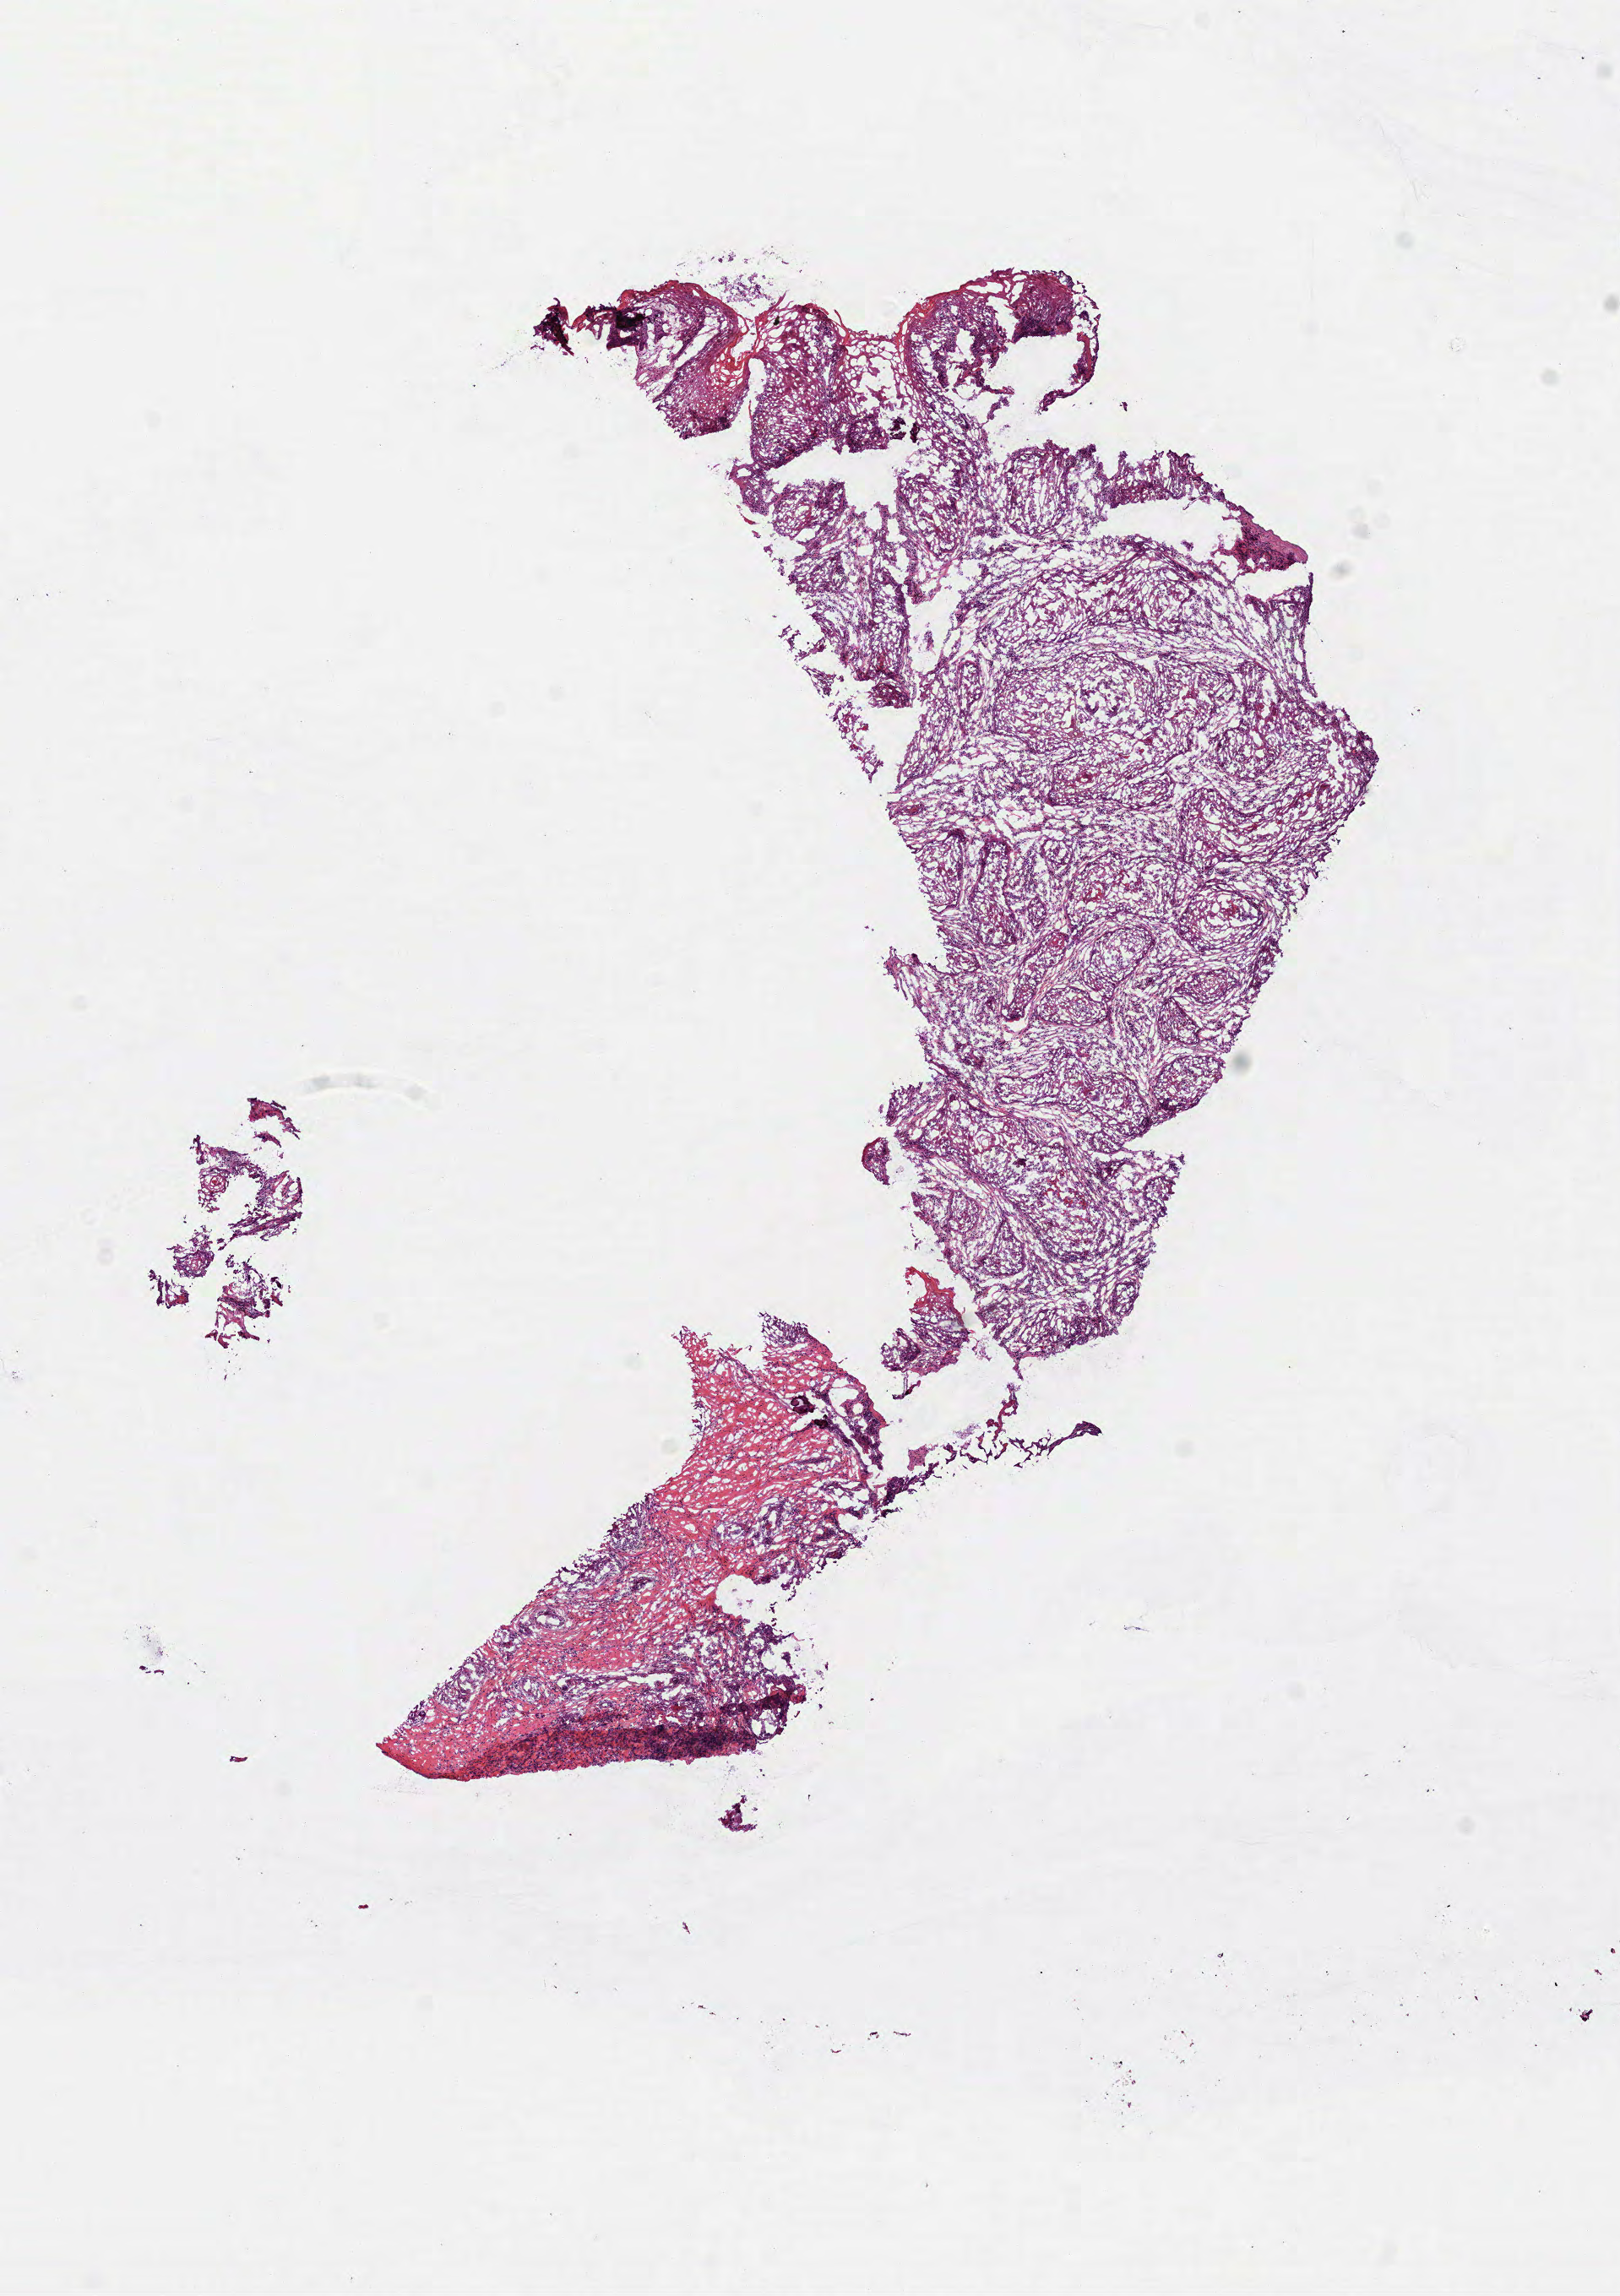
Whole-slide histology image, H&E, low-resolution overview of the scanned area, about 7.7 x 11.0 mm (acquisition: 40x scan); frozen section from the bottom of the tissue portion; head and neck, primary tumour sample. Male, age 87 years at initial diagnosis. Histologic grade: G1 (well differentiated). Composition of this section per pathologist review: tumour cells 75%, tumour nuclei 70%, normal cells 0%, stromal cells 20%, necrosis 5%. Inflammatory infiltration, as recorded: lymphocyte infiltration 5%, monocyte infiltration 0%, neutrophil infiltration 0%.
- AJCC pathologic stage: II (7th edition)
- TNM: T2 NX
- pathologic diagnosis: Squamous cell carcinoma, NOS